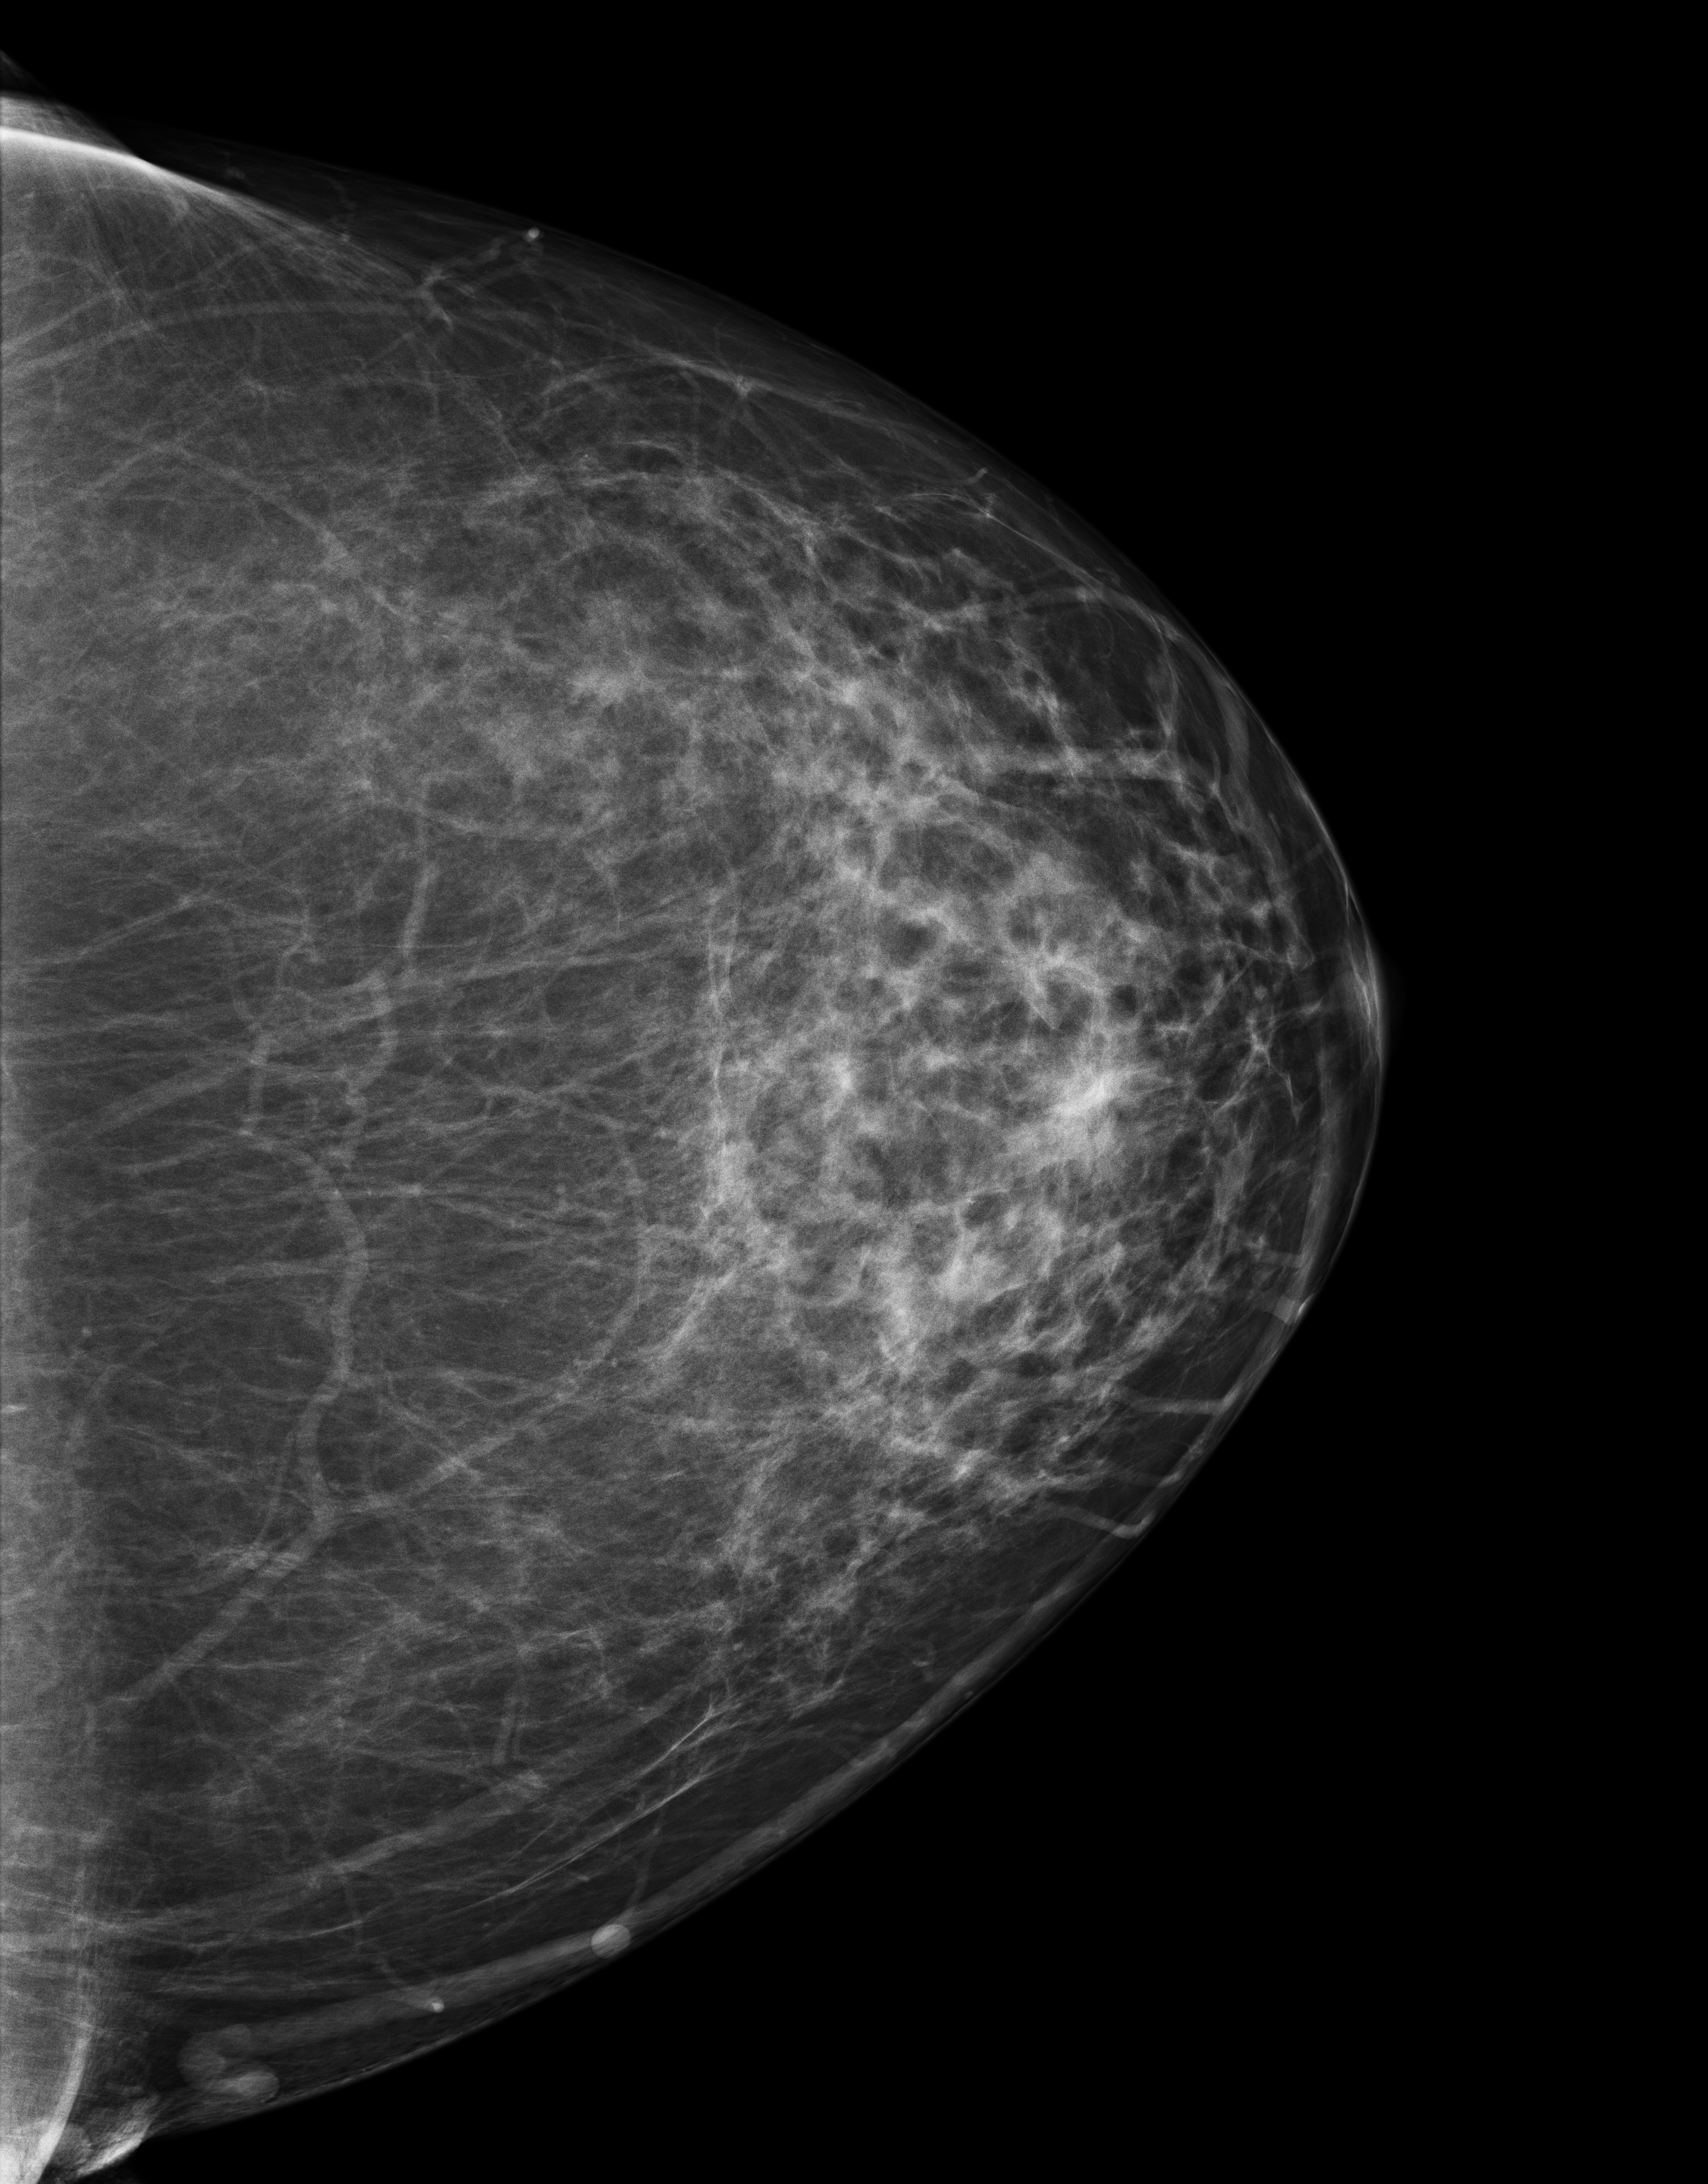
Screening examination; compressed breast thickness 86 mm. Female patient, age 59 years.
Image type: full-field digital mammogram. Breast: left. Projection: craniocaudal (CC) view.